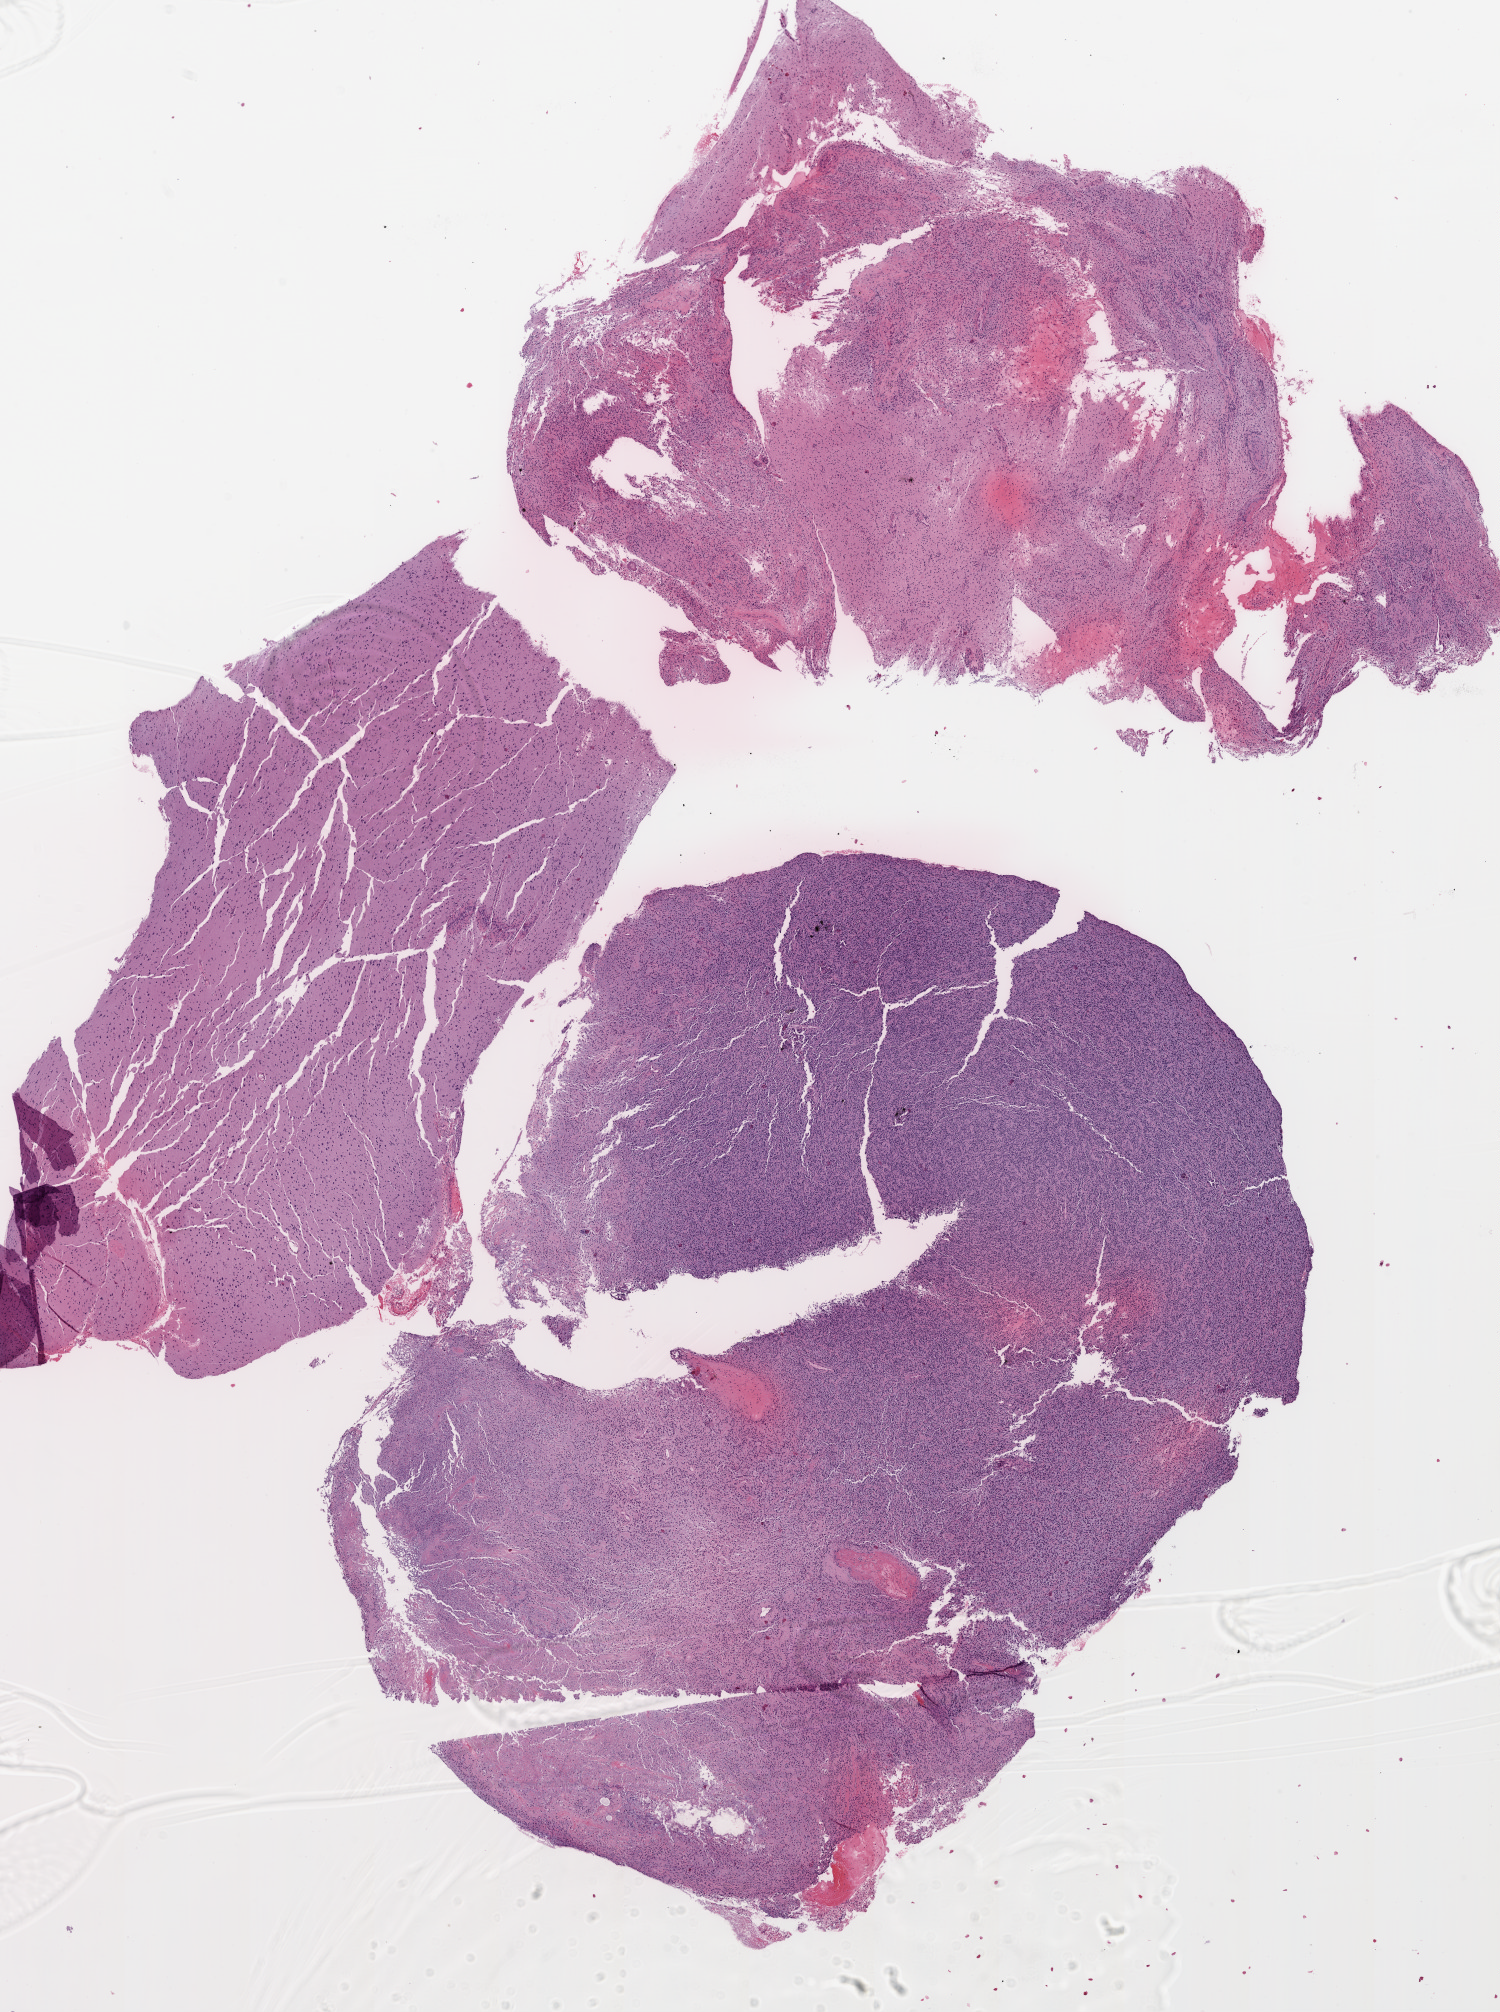
Digitized Hematoxylin and eosin (H&E) stained tissue section (whole slide), whole scanned area (about 12.0 x 16.1 mm, slide scanned at 20x) shown as a low-resolution overview. Formalin-fixed paraffin-embedded (FFPE) diagnostic section. Sample: primary tumour, brain. Male, age 57 years at initial diagnosis.
- diagnosis: Glioblastoma